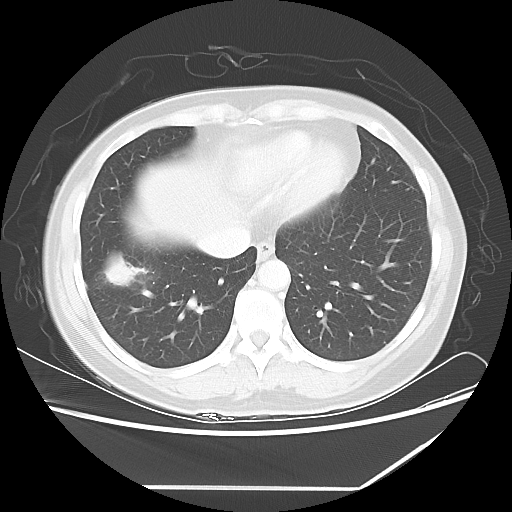
Chest CT, one axial slice; position 20 of 60 along the scan axis; reconstruction kernel LUNG; 100 kVp; lung window (W 1500 / L -600 HU); 5 mm slice thickness; 512 × 512 image matrix. Patient: female, 42 years. From the clinical record (not read from this slice): clinical TNM (as recorded): T2 N1 M0.
Outlined on this slice (rectangle marked by the reading radiologist):
- lung tumour (recorded histology: adenocarcinoma): bounding box <101,252,142,295> (left, top, right, bottom; pixels)